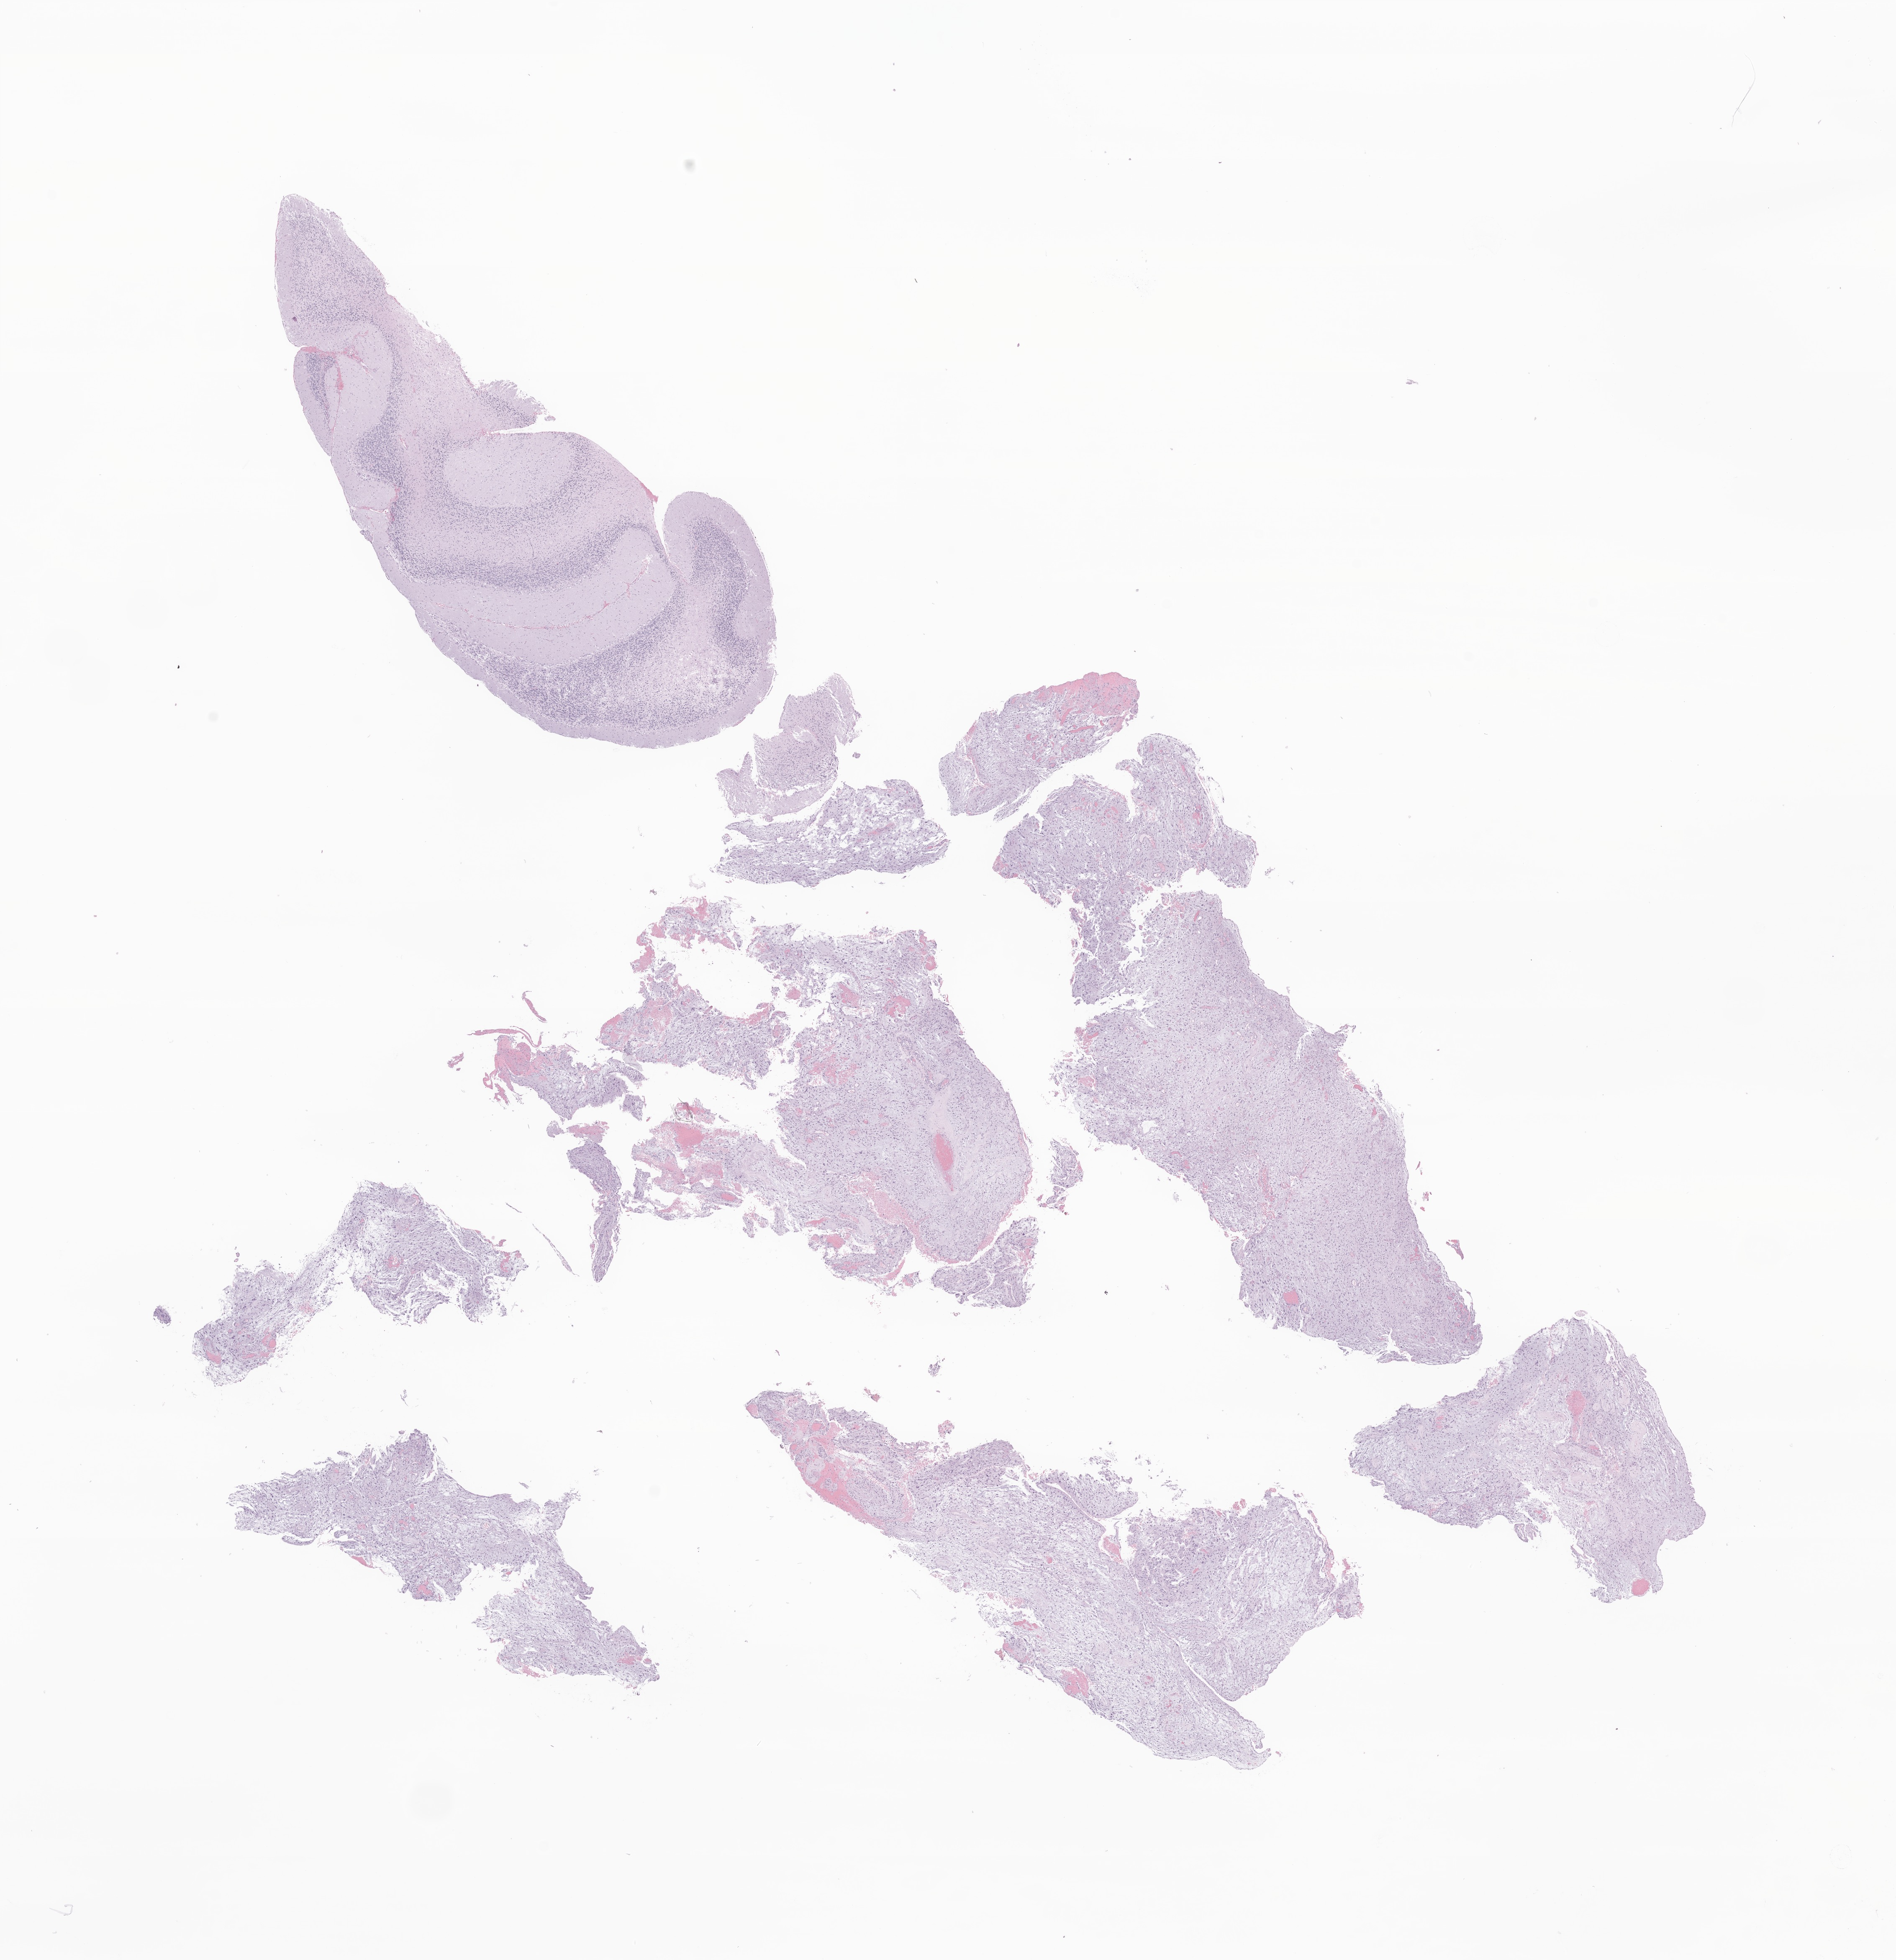
Haematoxylin and eosin whole-slide image of tumor tissue from the cerebellum, low-resolution overview of the scanned area, about 19.1 x 19.7 mm; FFPE section. Female patient, age 72 months.
Diagnosis: Pilocytic astrocytoma.